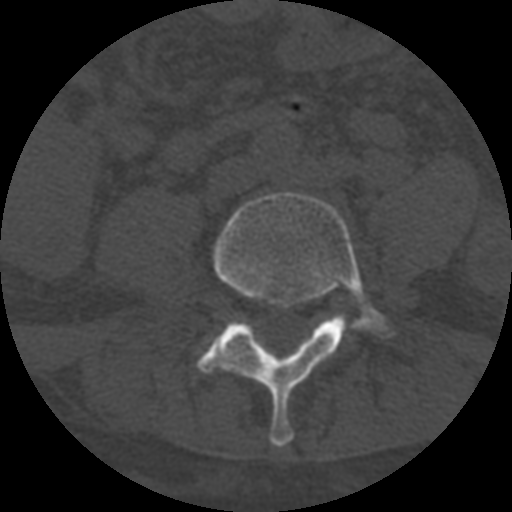
CT including the spine, one axial slice; slice 204 of 708 in the series (ordered by position); reconstruction kernel STANDARD; one of 3 acquisitions stored at this slice position; bone window (W 1800 / L 400 HU); 512 × 512 image matrix. Patient age 55 years. Case-level facts recorded for this patient, not image findings: primary cancer: colon; vertebrae with lytic lesions (as recorded): T12, L1, L5.
Outlined on this slice (semi-automatically segmented with operator editing):
- L4 vertebra: bounding box (x1, y1, x2, y2) in pixels: (197, 192, 387, 447)
- L5 vertebra: (221, 316, 345, 336)